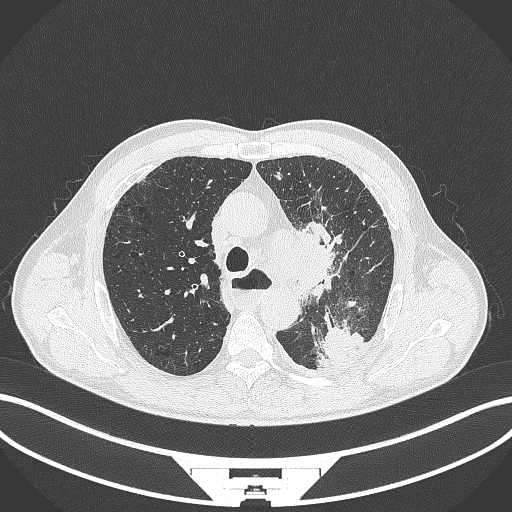
Chest CT, one axial slice. Slice 273 of 411 in the series (ordered by position). Reconstruction kernel B70f. Lung window (W 1500 / L -600 HU). 1 mm slice thickness. 512 × 512 image matrix. Patient: male, 57 years. From the clinical record (not read from this slice): clinical TNM (as recorded): T2a N1 M0.
Annotated regions visible in this slice (rectangle marked by the reading radiologist):
- lung tumour (recorded histology: squamous cell carcinoma): box from (x=290, y=224) to (x=337, y=300) px